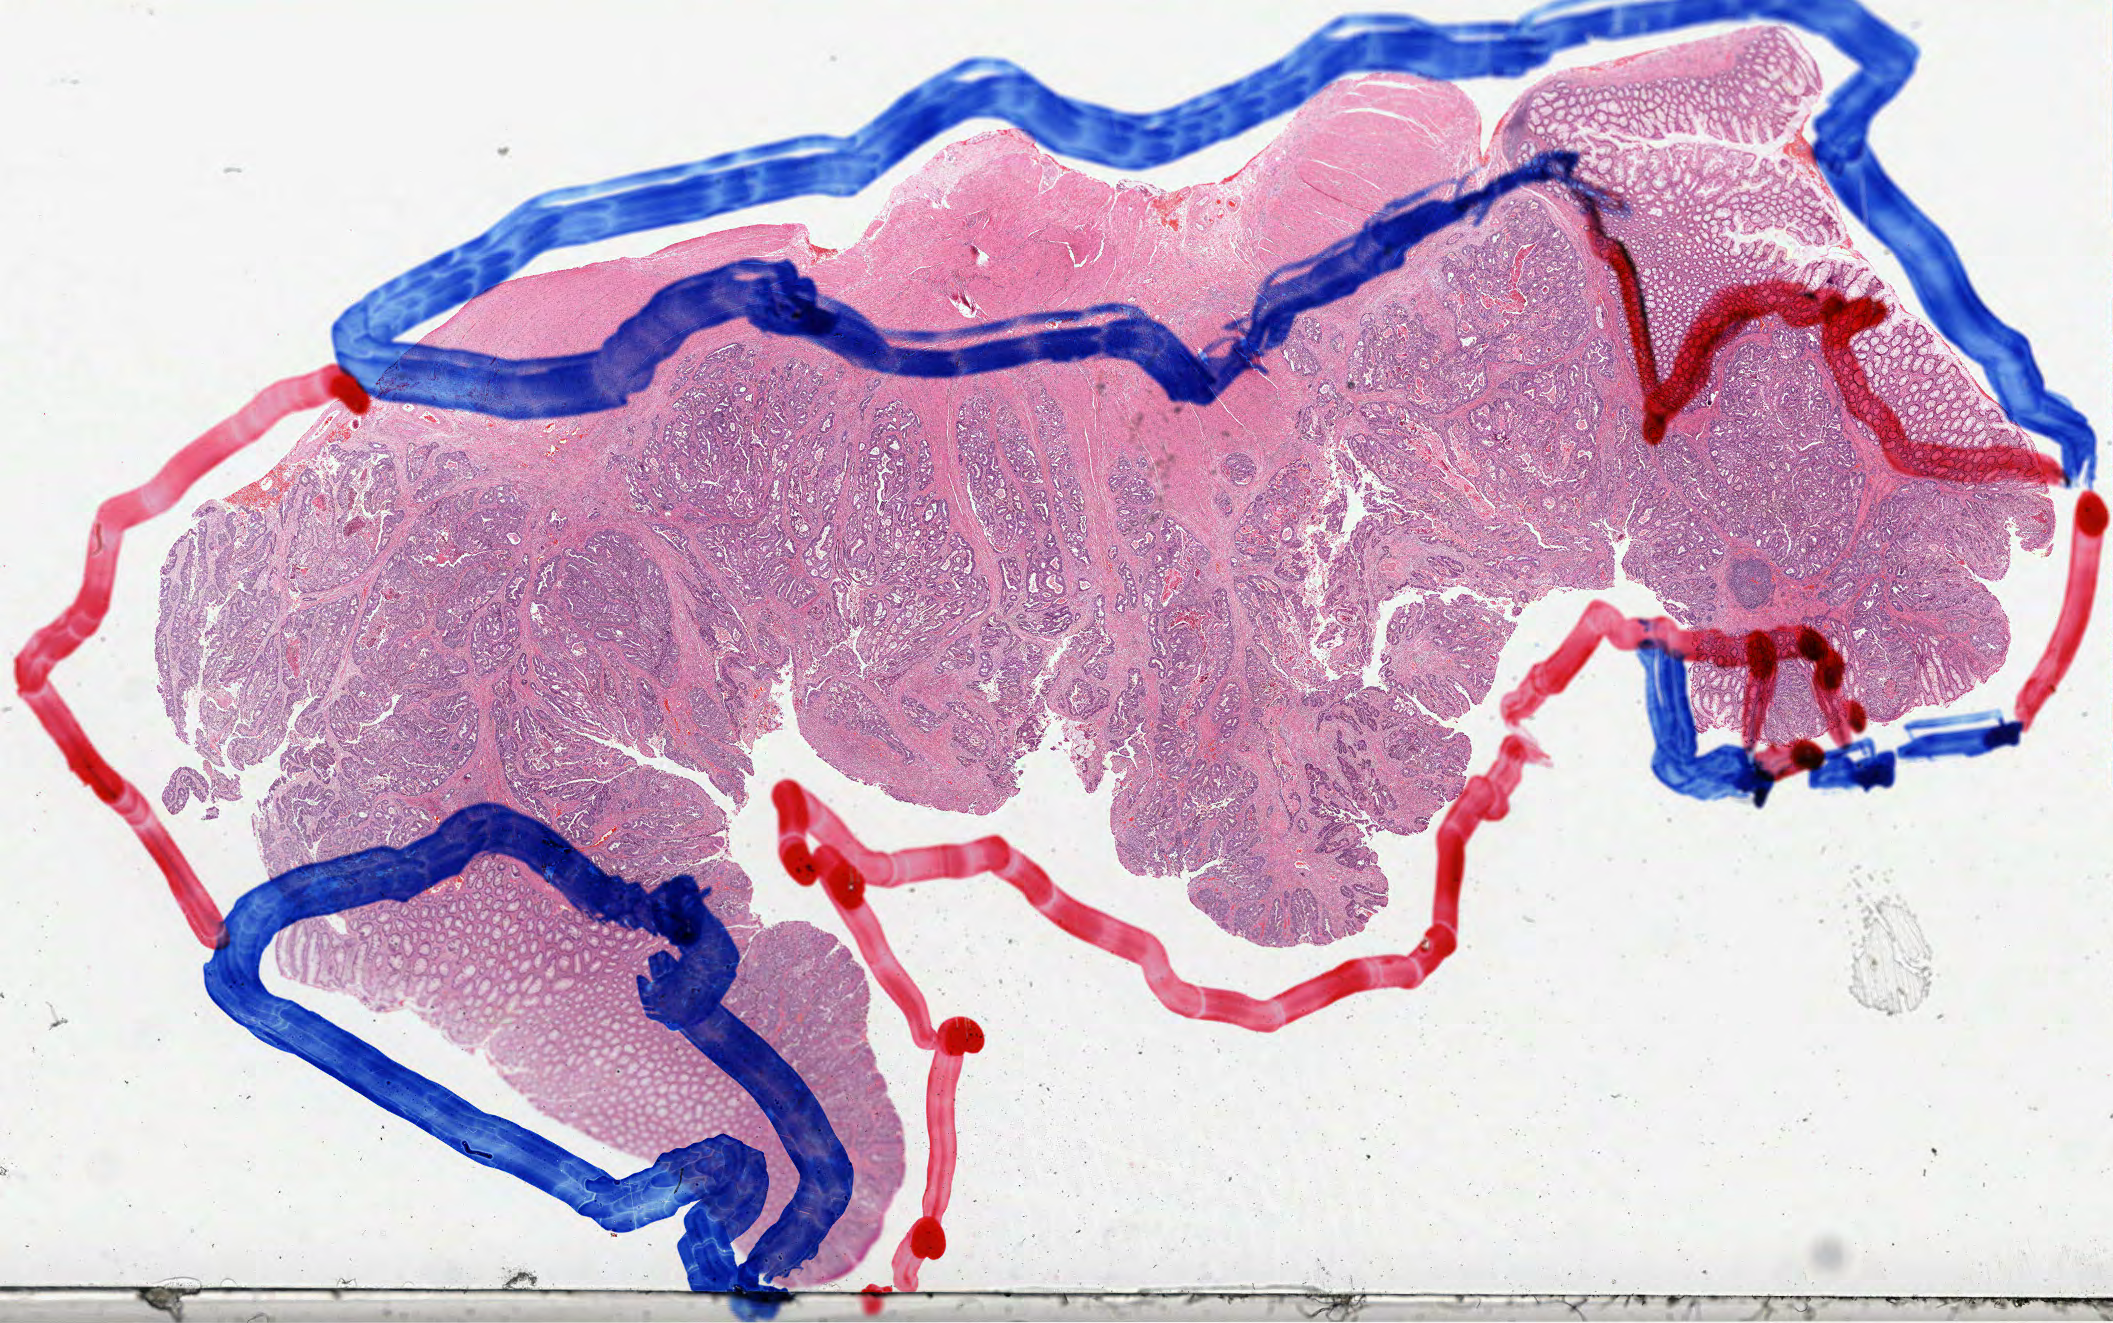
H&E-stained whole-slide image — whole scanned area (about 34.1 x 21.3 mm) shown as a low-resolution overview.
Specimen: formalin-fixed paraffin-embedded (FFPE) diagnostic section; rectum, primary tumour sample.